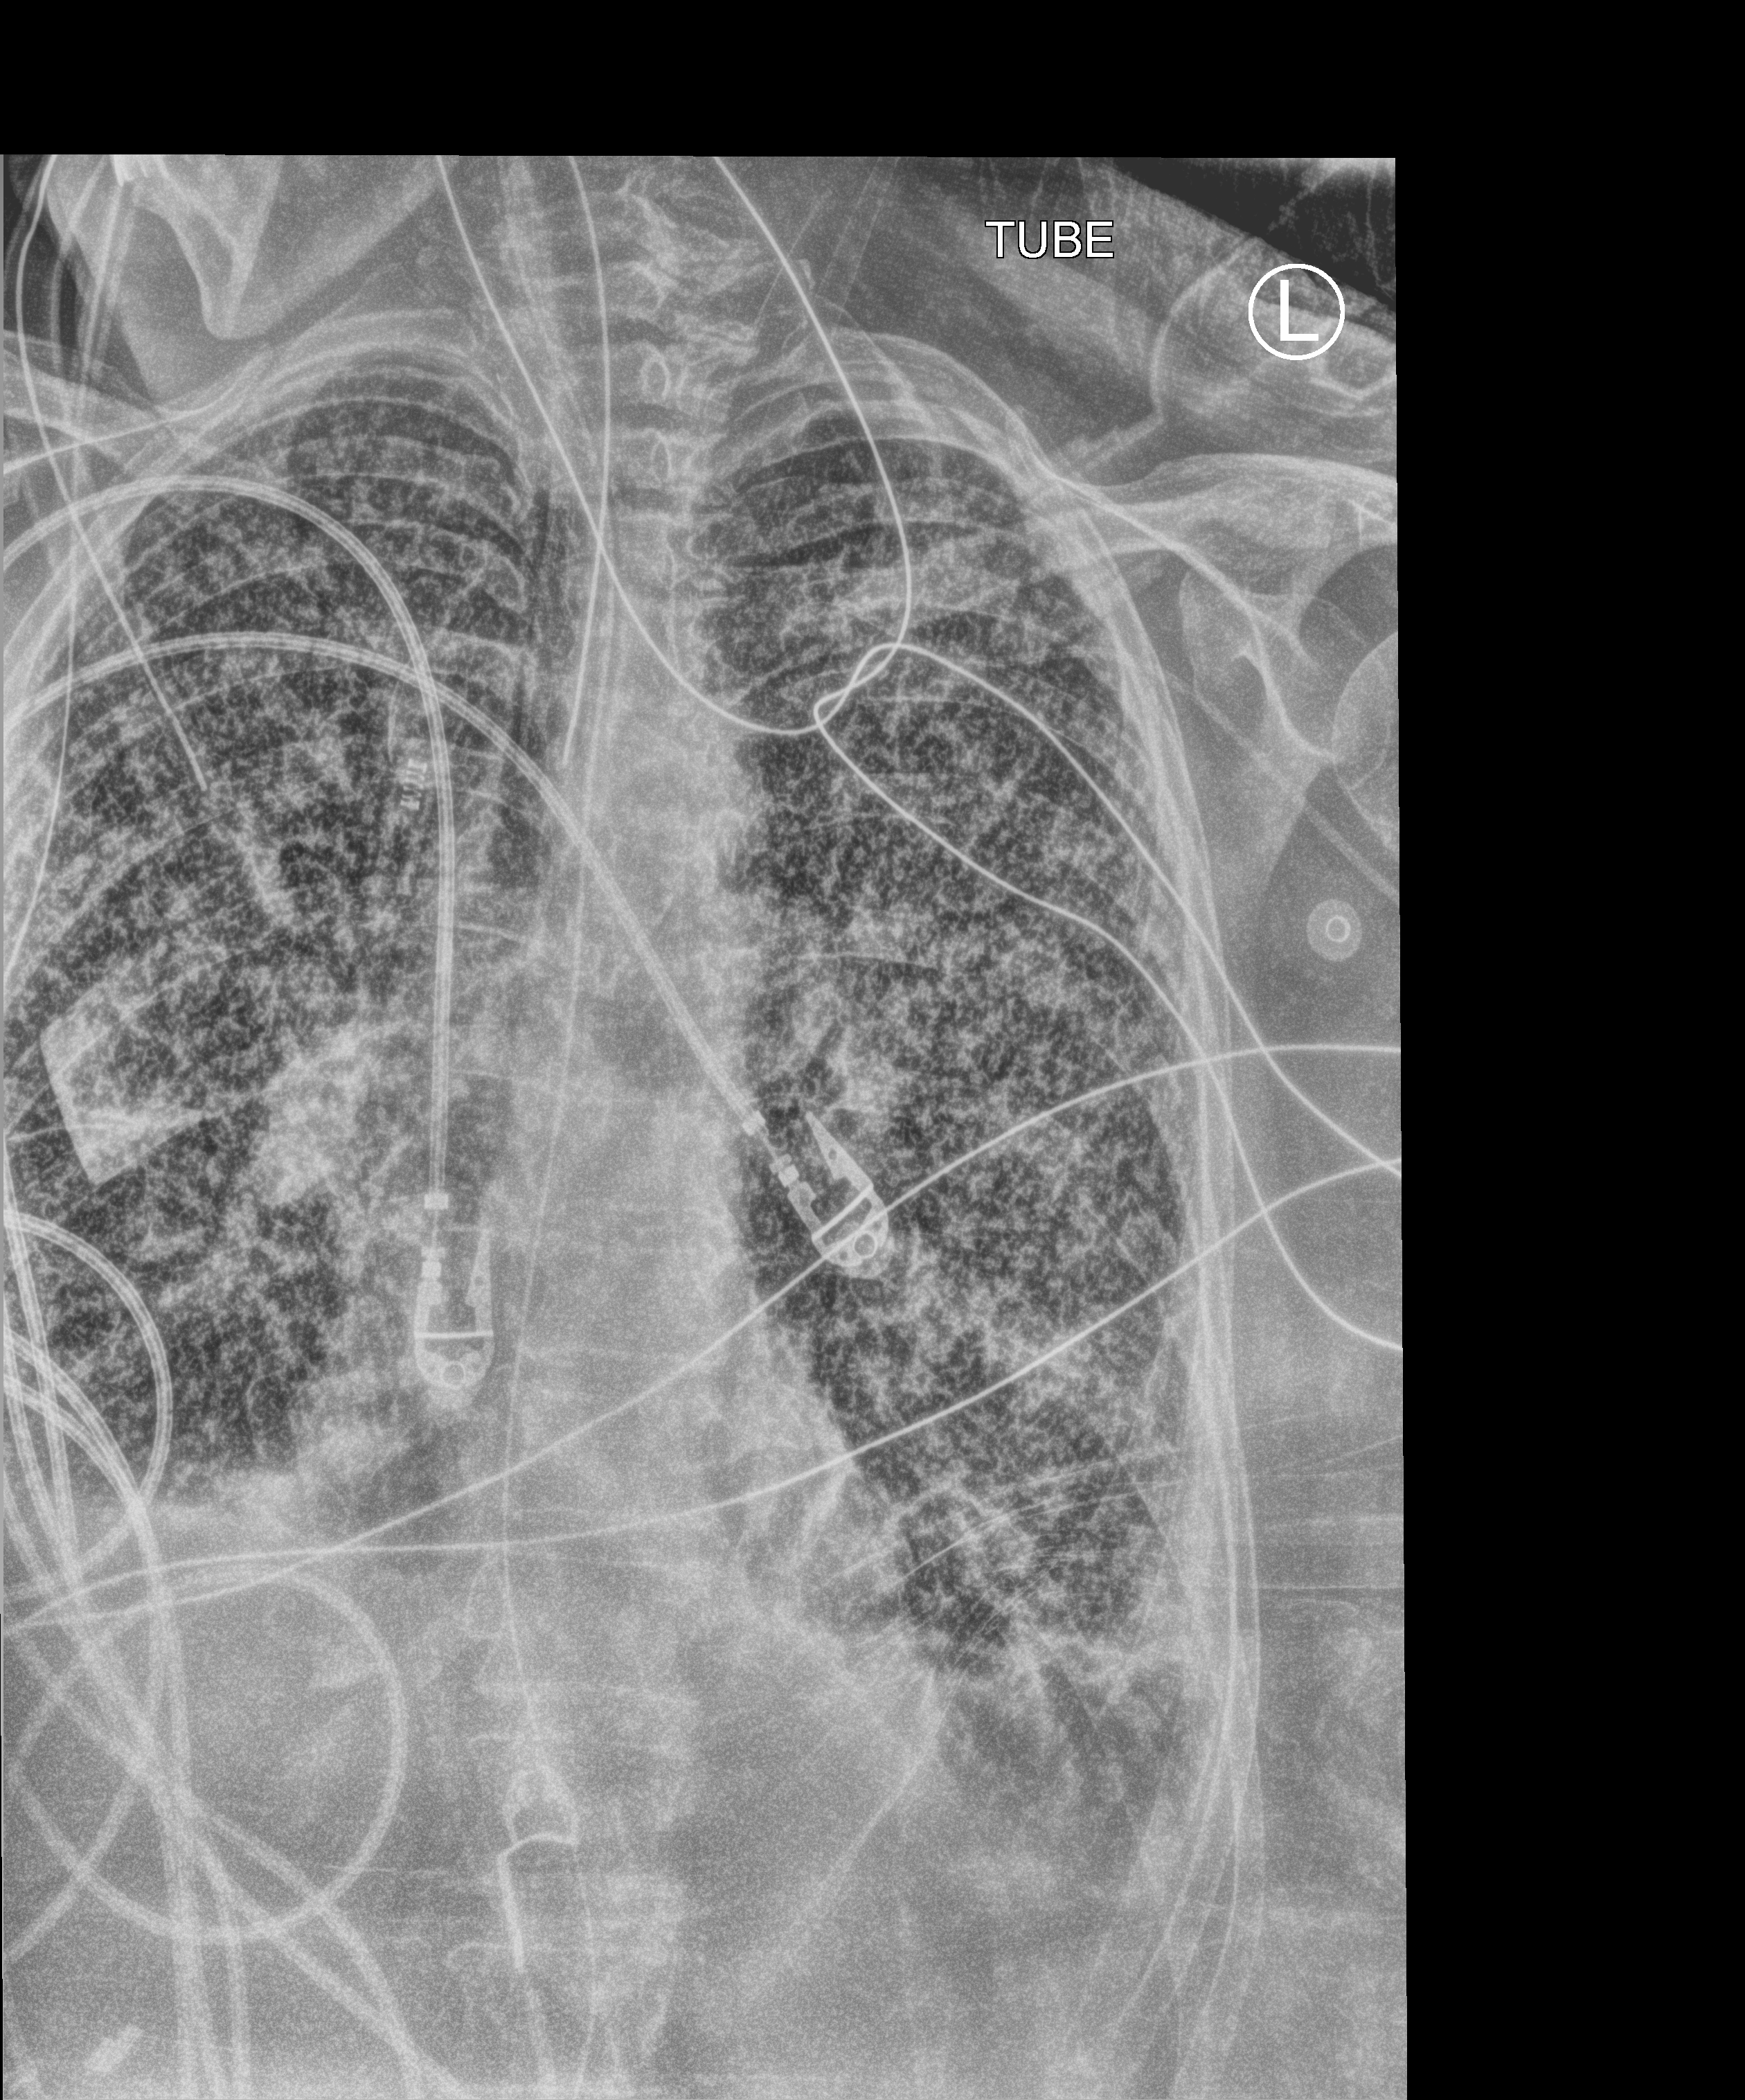
Chest X-ray (portable), anteroposterior (AP) projection. Patient hospitalised with COVID-19; female, aged 60–74 years.
Hospital-stay facts (about this admission, not read from this image; timing relative to this image not recorded): mechanically ventilated during this hospital stay: yes; length of hospital stay: 19 days.